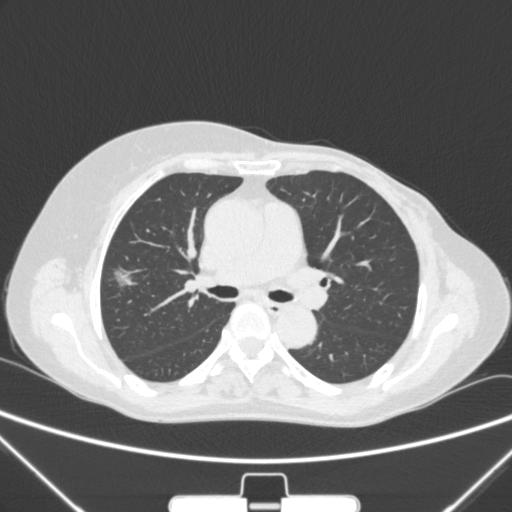
Chest CT, one axial slice; lung window (W 1500 / L -600 HU); 1 mm slice thickness; 512 × 512 image matrix, field of view 350 × 350 mm. Patient: female, 64 years. Case-level facts recorded for this patient, not image findings: clinical TNM (as recorded): T1c N0 M0; histopathological grade: G1-2.
Outlined on this slice (rectangle marked by the reading radiologist):
- lung tumour (recorded histology: adenocarcinoma): box from (x=104, y=261) to (x=151, y=306) px